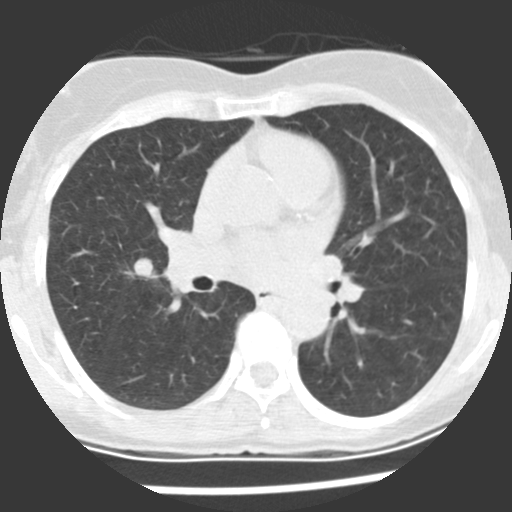
Axial slice from a low-dose chest CT screening exam; baseline screening round; lung window (W 1500 / L -600 HU); 2.5 mm slice thickness; slice 107 of 225 in the series; 512 × 512 image matrix. Female participant, aged 60 years at enrolment.
• Lesion marked by an expert reader, bounding box [x1, y1, x2, y2] px = [116, 251, 175, 296].
• The screening reader recorded 2 non-calcified nodules or masses ≥4 mm on this exam (right upper lobe, right middle lobe); which of them this box marks is not recorded.